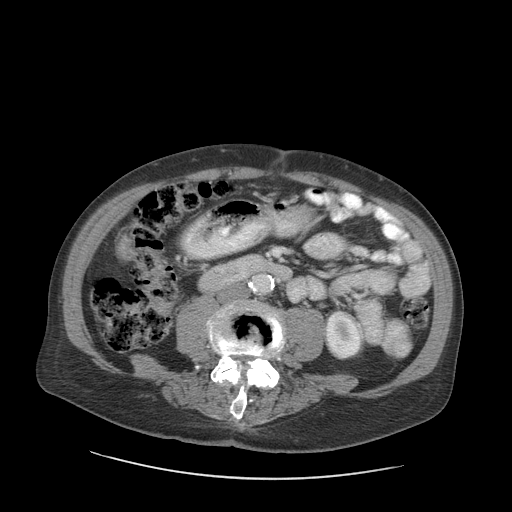
Contrast-enhanced abdominal CT (liver protocol), one axial slice. Slice 16 of 89 in the series (ordered by position). Reconstruction kernel STANDARD. 140 kVp. Soft-tissue window (W 400 / L 40 HU). 512 × 512 image matrix, field of view 420 × 420 mm. Case-level facts recorded for this patient, not image findings: diagnosis: hepatocellular carcinoma (patient treated with transarterial chemoembolisation; whether this scan precedes or follows treatment is not stated here); TNM stage (as recorded): Stage-I; Child-Pugh class: A; tumour differentiation: moderately differentiated.
Structures marked on this image (semi-automatic segmentation, software-assisted and operator-edited):
- liver parenchyma outside the tumour (the mass and vessels are separate outlines, so this box may not span the whole liver): bounding box <118,238,128,256> (left, top, right, bottom; pixels)